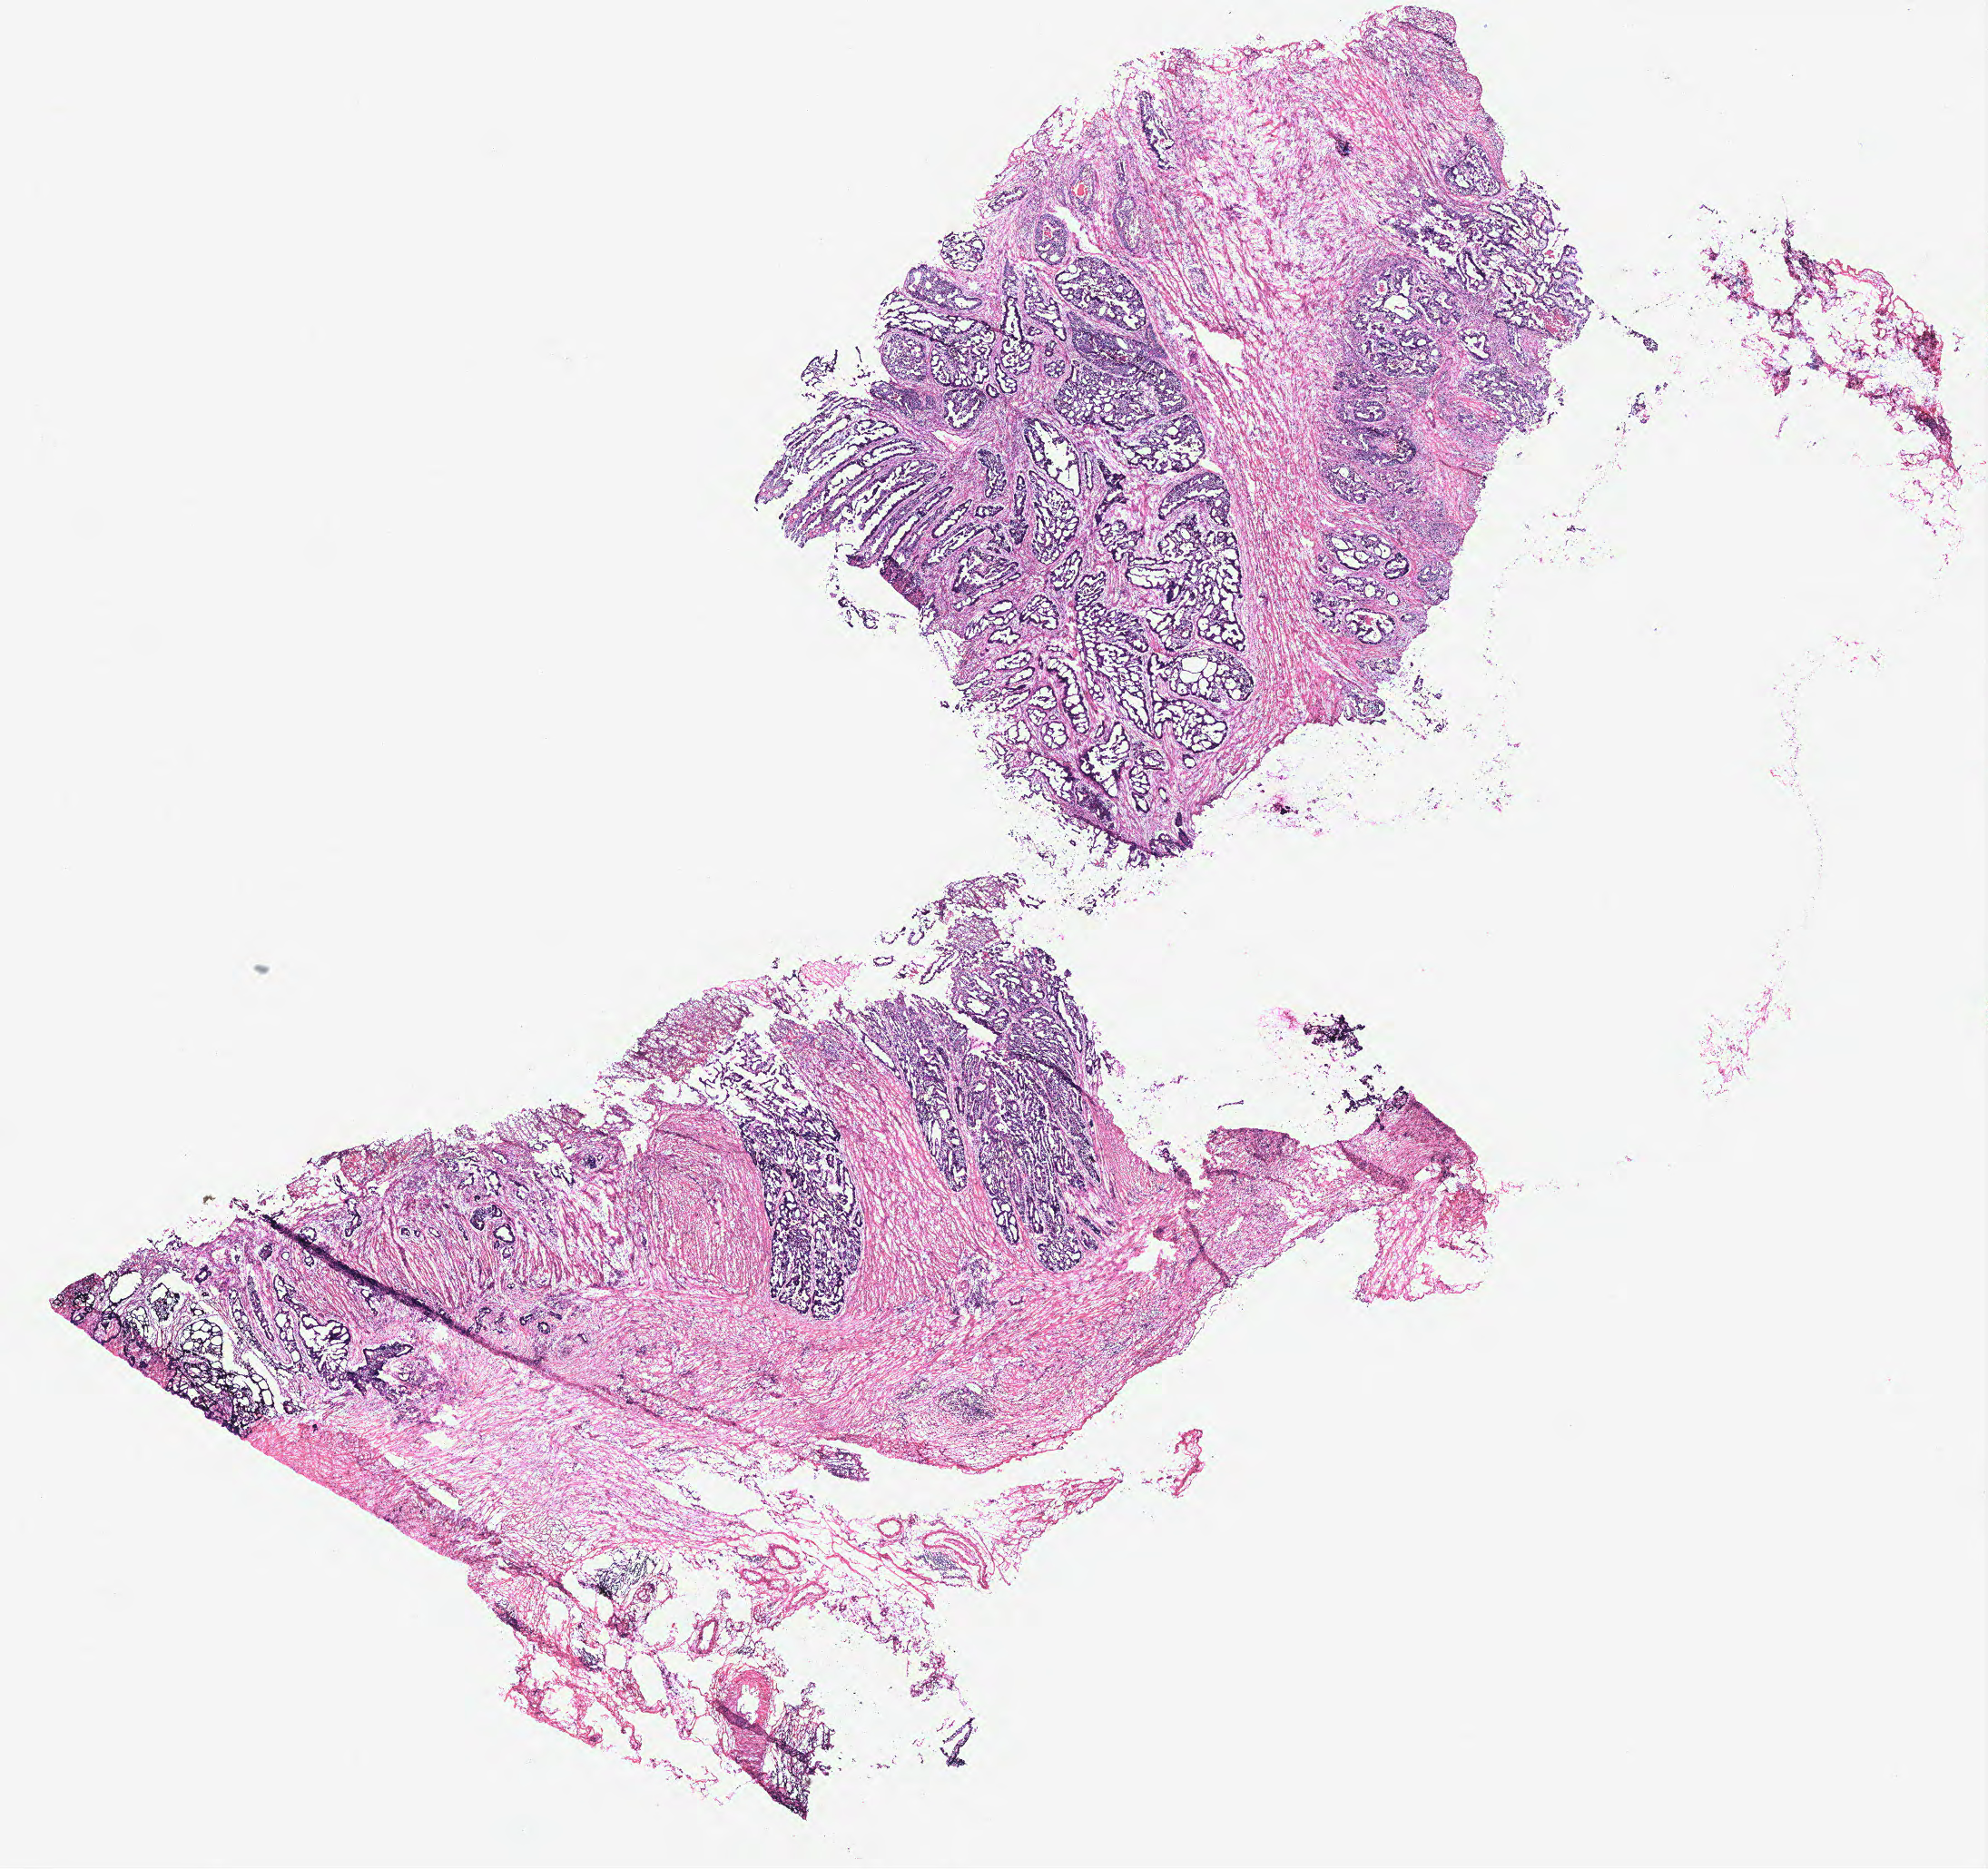
H&E whole-slide image, shown as a low-resolution overview of the whole scanned area (about 17.5 x 16.5 mm, slide scanned at 40x), colon, normal (non-tumour) tissue. 67-year-old male patient.
This section: normal (non-tumour) tissue from the same patient. Patient diagnosis: Adenocarcinoma, NOS.